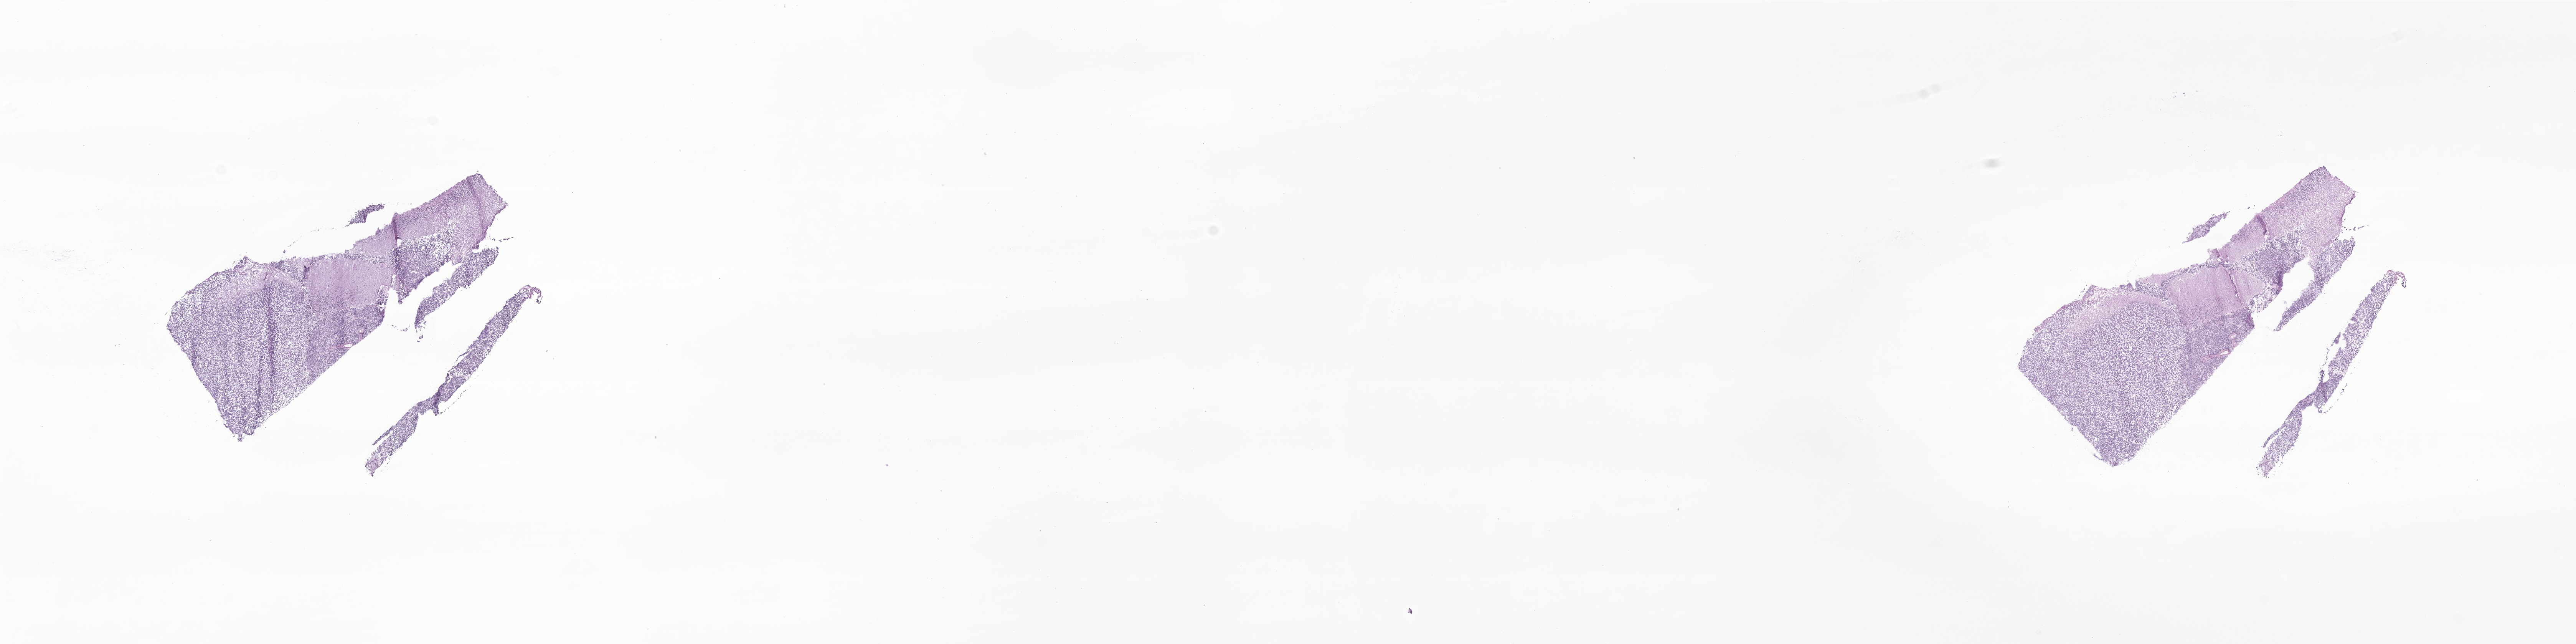
Digitized haematoxylin and eosin-stained section of tumor tissue from the brain, whole scanned area (about 28.3 x 7.1 mm) shown as a low-resolution overview, frozen section (OCT-embedded). Patient: male, age 71 months (5 years 11 months).
Recorded diagnosis: Medulloblastoma, NOS.